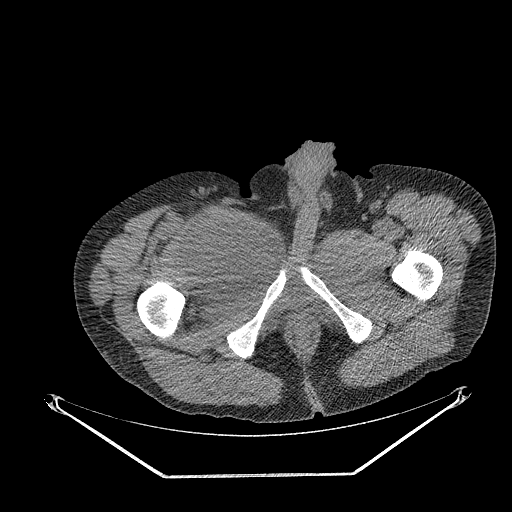
CT of an extremity soft-tissue mass (from a PET/CT study), one axial slice; soft-tissue window (W 400 / L 40 HU); 512 × 512 image matrix. Male patient. Case-level facts recorded for this patient, not image findings: histological type: undifferentiated - pleiomorphic; grade: high; site of the primary tumour: right thigh.
Outlined on this slice (expert contour drawn on MRI and transferred to this co-registered scan by the dataset authors):
- gross tumour volume including surrounding oedema: bounding box <203,210,257,263> (left, top, right, bottom; pixels)
- gross tumour volume (mass): <206,219,247,257>